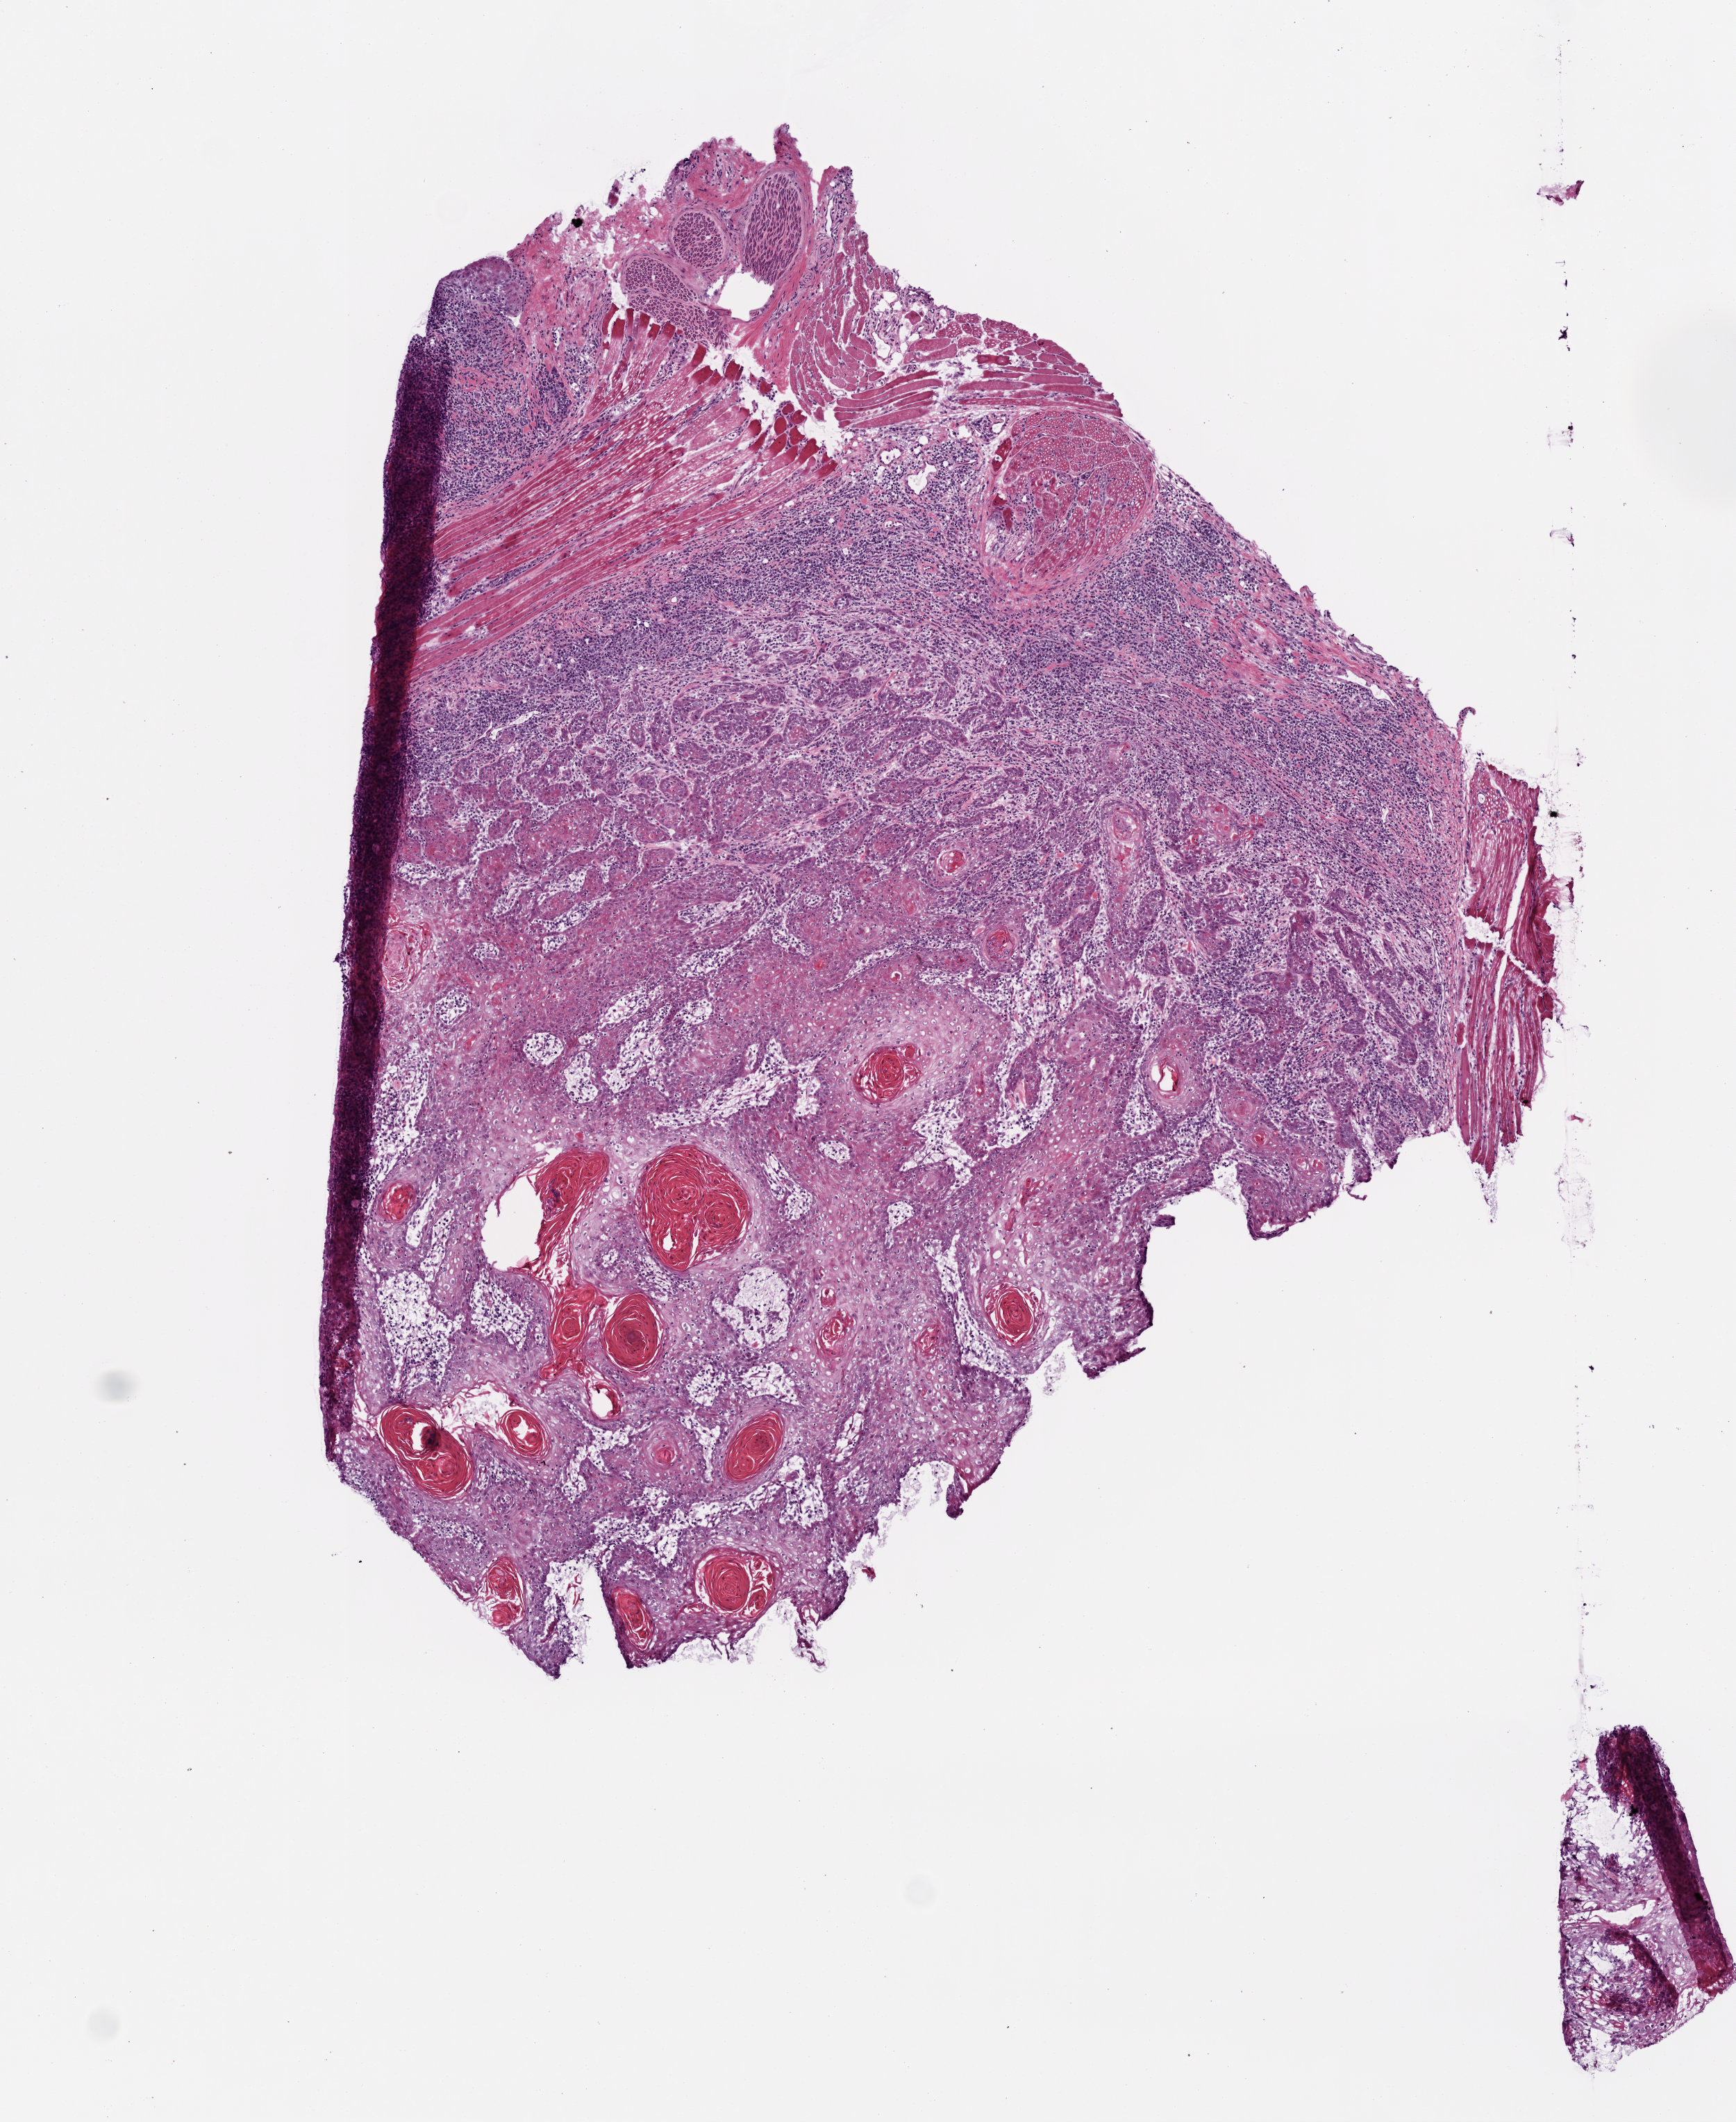
Digitized Hematoxylin and eosin (H&E) stained tissue section (whole slide) — a low-resolution overview of the entire scanned area, about 5.0 x 6.1 mm (acquisition: 20x scan). Frozen section from the top of the tissue portion. Primary tumour sample from the head and neck. Male, age 65 years at initial diagnosis. Histologic grade: G2 (moderately differentiated). Slide review estimates, as recorded: tumour cells 70%, tumour nuclei 70%, normal cells 25%, stromal cells 0%, necrosis 5%. Inflammatory infiltration, as recorded: lymphocyte infiltration 25%, neutrophil infiltration 2%.
- AJCC pathologic stage: I (6th edition)
- lymph nodes positive (case pathology): 0 of 22 examined
- pathologic diagnosis: Squamous cell carcinoma, NOS (tongue, NOS)